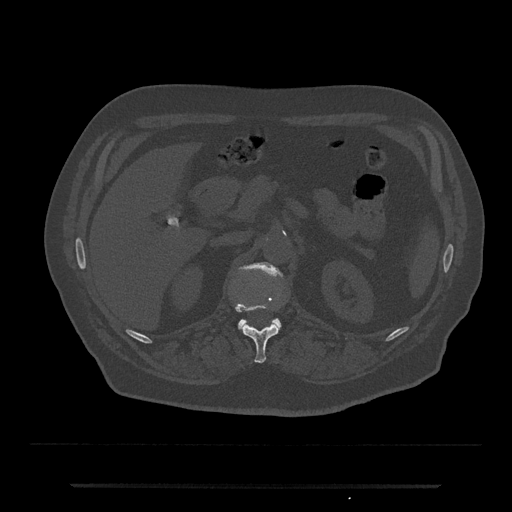
CT including the spine, one axial slice. Position 573 of 797 along the scan axis. Bone window (W 1800 / L 400 HU). 0.5 mm slice thickness. 512 × 512 image matrix. Patient: male, 80 years. From the clinical record (not read from this slice): primary cancer: prostate.
Annotated regions visible in this slice (semi-automatic segmentation, software-assisted and operator-edited):
- L1 vertebra: bounding box [x1, y1, x2, y2] px = [237, 262, 283, 330]
- T12 vertebra: [235, 302, 280, 363]